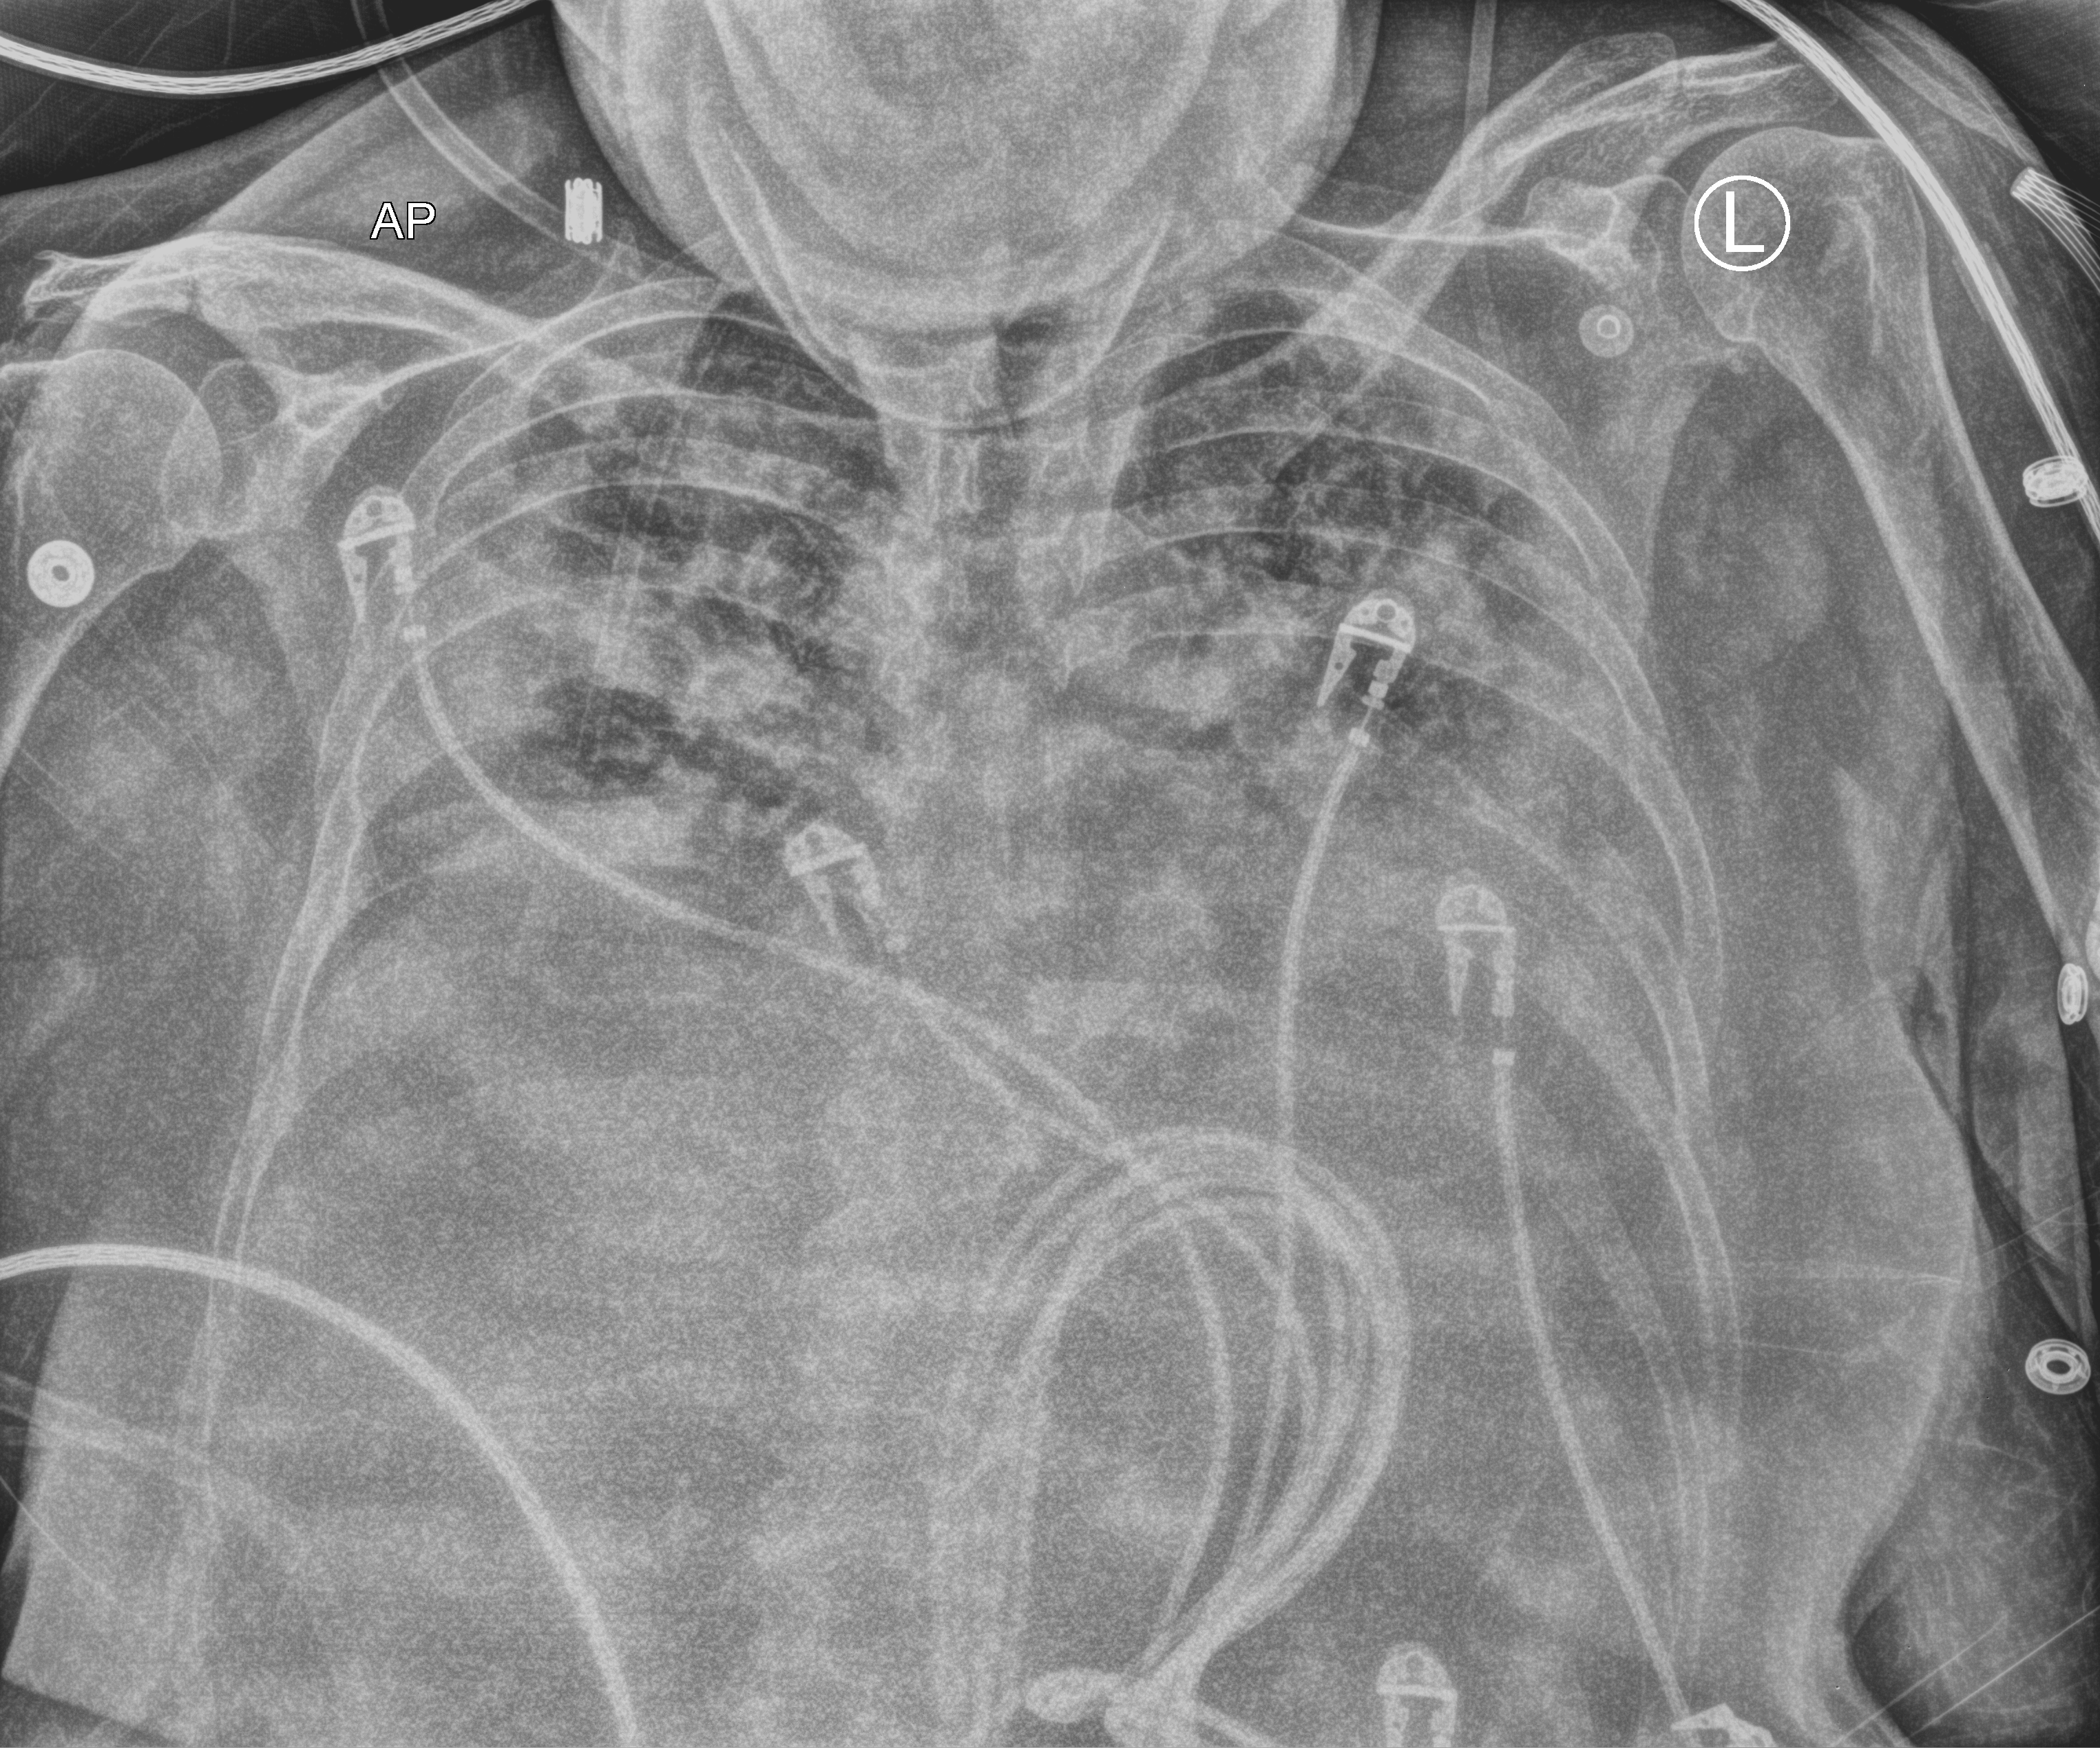
Bedside chest radiograph (computed radiography). Female patient hospitalised with COVID-19, age 18–59 years.
Hospital-stay facts (about this admission, not read from this image; timing relative to this image not recorded):
- mechanically ventilated during this hospital stay: no
- admitted to intensive care during this hospital stay: yes
- COPD (admission record): no